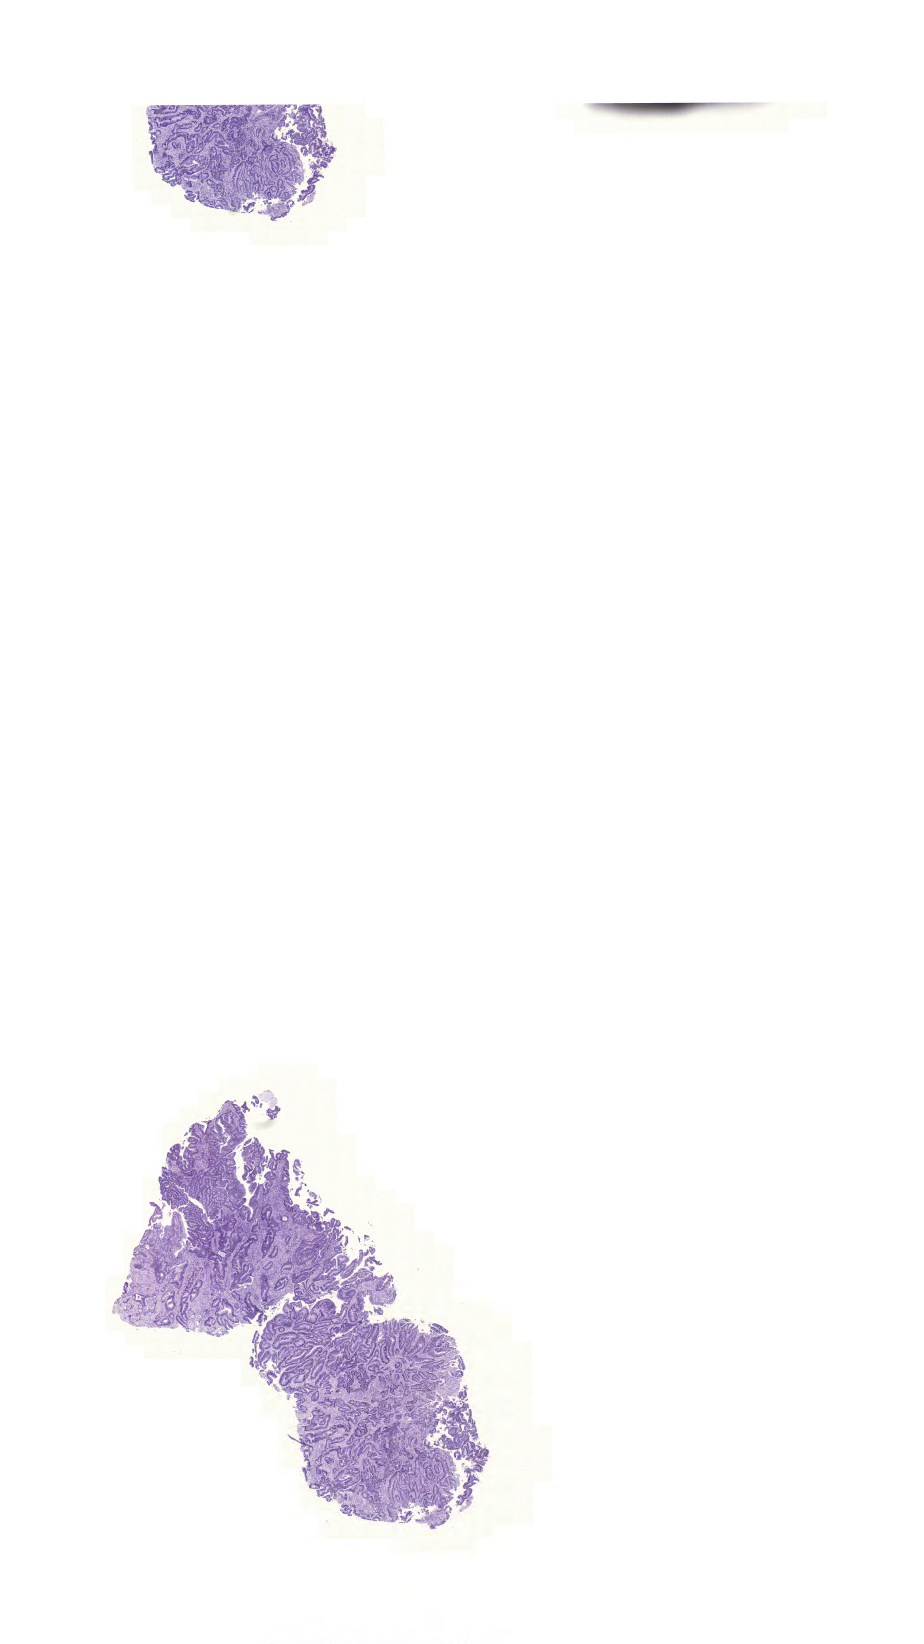
Digitized Hematoxylin and eosin (H&E) stained tissue section (whole slide), whole scanned area (about 13.7 x 24.5 mm, from a 20x scan) shown as a low-resolution overview. Formalin-fixed paraffin-embedded (FFPE) diagnostic section. Primary tumour sample from the rectum. Male, age 74 years at initial diagnosis.
• pathologic diagnosis: Adenocarcinoma, NOS (rectosigmoid junction)
• AJCC pathologic stage: IIIB
• lymph nodes positive (case pathology): 1 of 14 examined
• TNM: T3 N1 M0